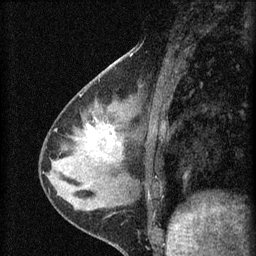
Breast MRI (dynamic contrast-enhanced), one sagittal slice; position 22 of 60 along the scan axis; dynamic contrast-enhanced series, image 2 of 4 at this slice position (ordered by acquisition); 1.5 T; TE 4.2 ms, TR 8.2 ms; 2 mm slice thickness; 256 × 256 image matrix. Patient: female, 37 years.
Structures marked on this image (semi-automatically segmented with operator editing):
- analysis volume of interest (the breast-tissue region the enhancement analysis was run in; not a lesion): box from (x=77, y=116) to (x=127, y=175) px
- tumour enhancement mask (voxels above the 70 % enhancement threshold inside the analysis volume of interest): (x=87, y=124)–(x=115, y=141)